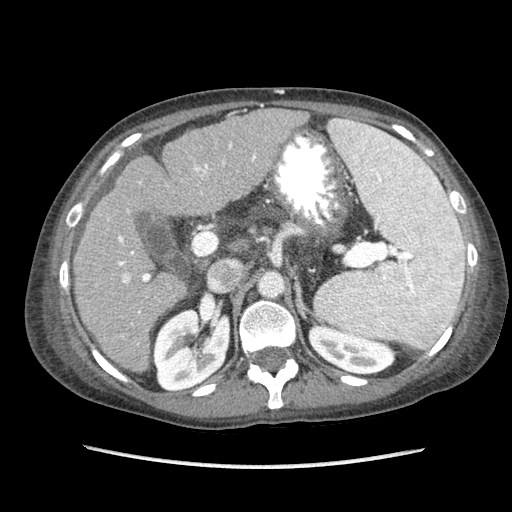
Contrast-enhanced abdominal CT (liver protocol), one axial slice; soft-tissue window (W 400 / L 40 HU); 2.5 mm slice thickness; 512 × 512 image matrix, field of view 340 × 340 mm. From the clinical record (not read from this slice): diagnosis: hepatocellular carcinoma (patient treated with transarterial chemoembolisation; whether this scan precedes or follows treatment is not stated here); TNM stage (as recorded): Stage-IIIB; Child-Pugh class: A; tumour differentiation: no biopsy; tumour nodularity: uninodular.
Structures marked on this image (semi-automatic segmentation, software-assisted and operator-edited):
- liver parenchyma outside the tumour (the mass and vessels are separate outlines, so this box may not span the whole liver): bounding box [x1, y1, x2, y2] px = [72, 108, 308, 372]
- liver vessels: [118, 143, 256, 325]